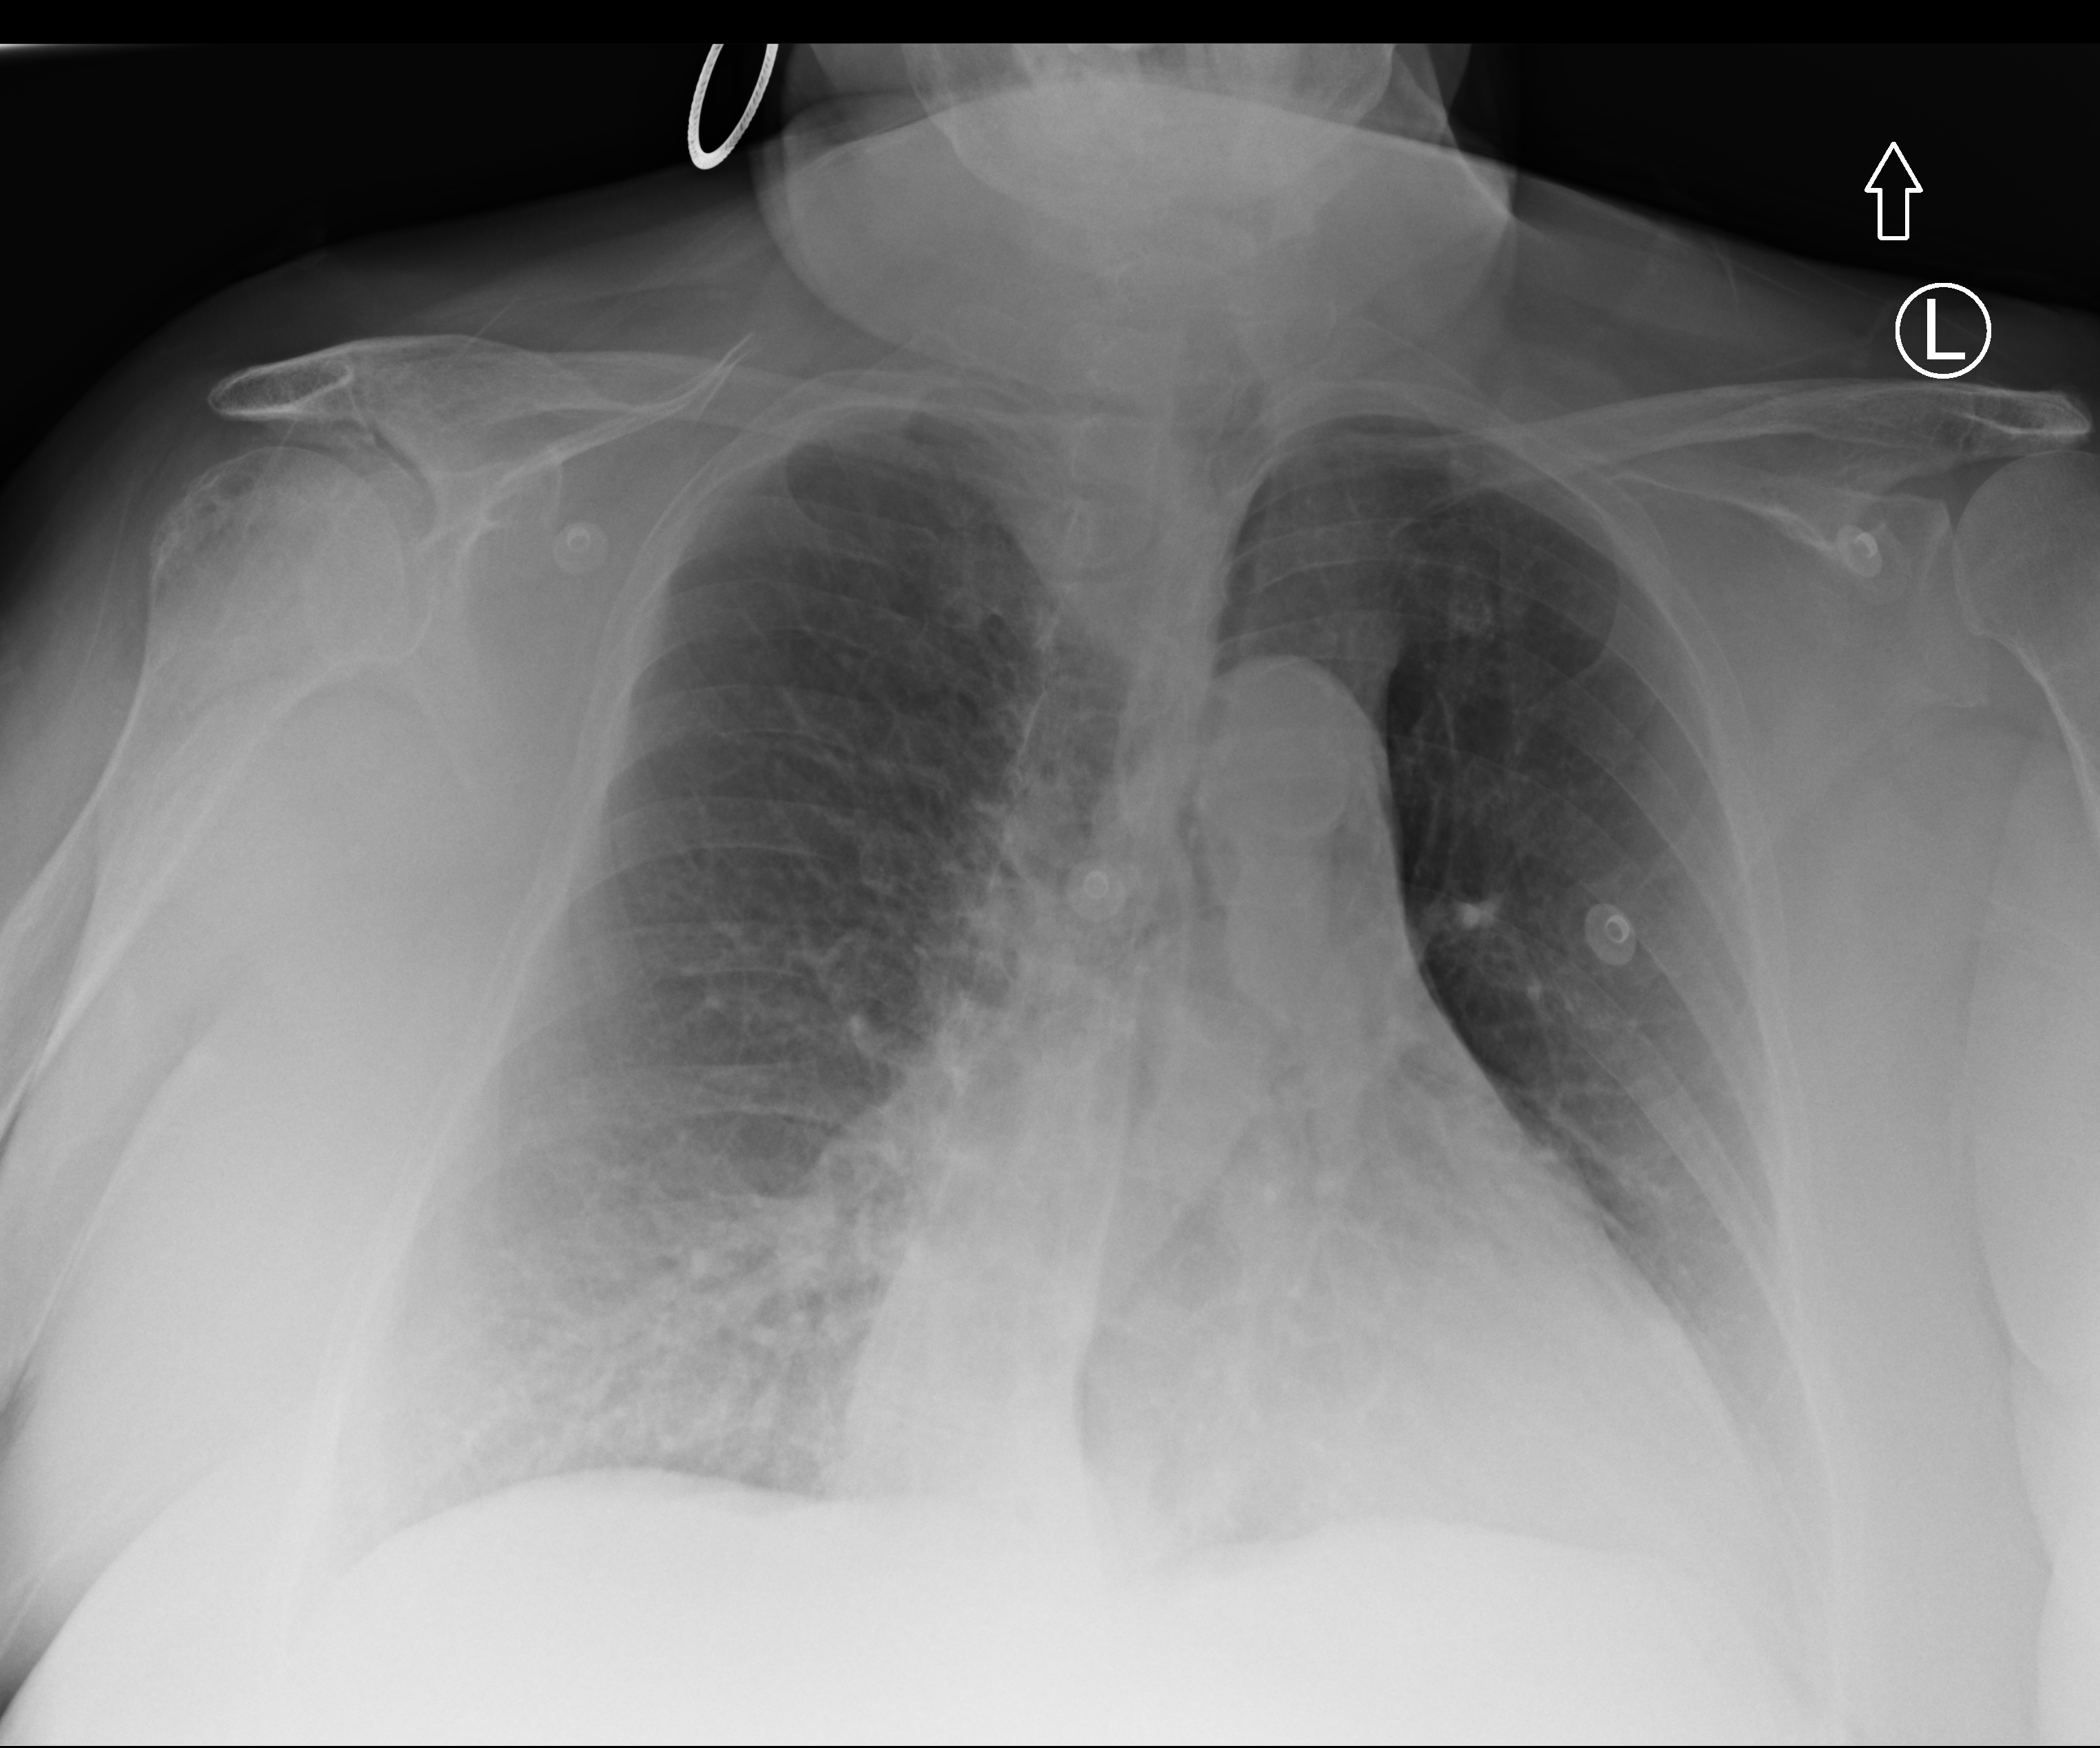
Bedside chest radiograph (computed radiography); anteroposterior (AP) projection. Patient hospitalised with COVID-19; female, aged 60–74 years.
Hospital-stay facts (about this admission, not read from this image; timing relative to this image not recorded):
- admitted to intensive care during this hospital stay: yes
- length of hospital stay: 9 days
- mechanically ventilated during this hospital stay: no